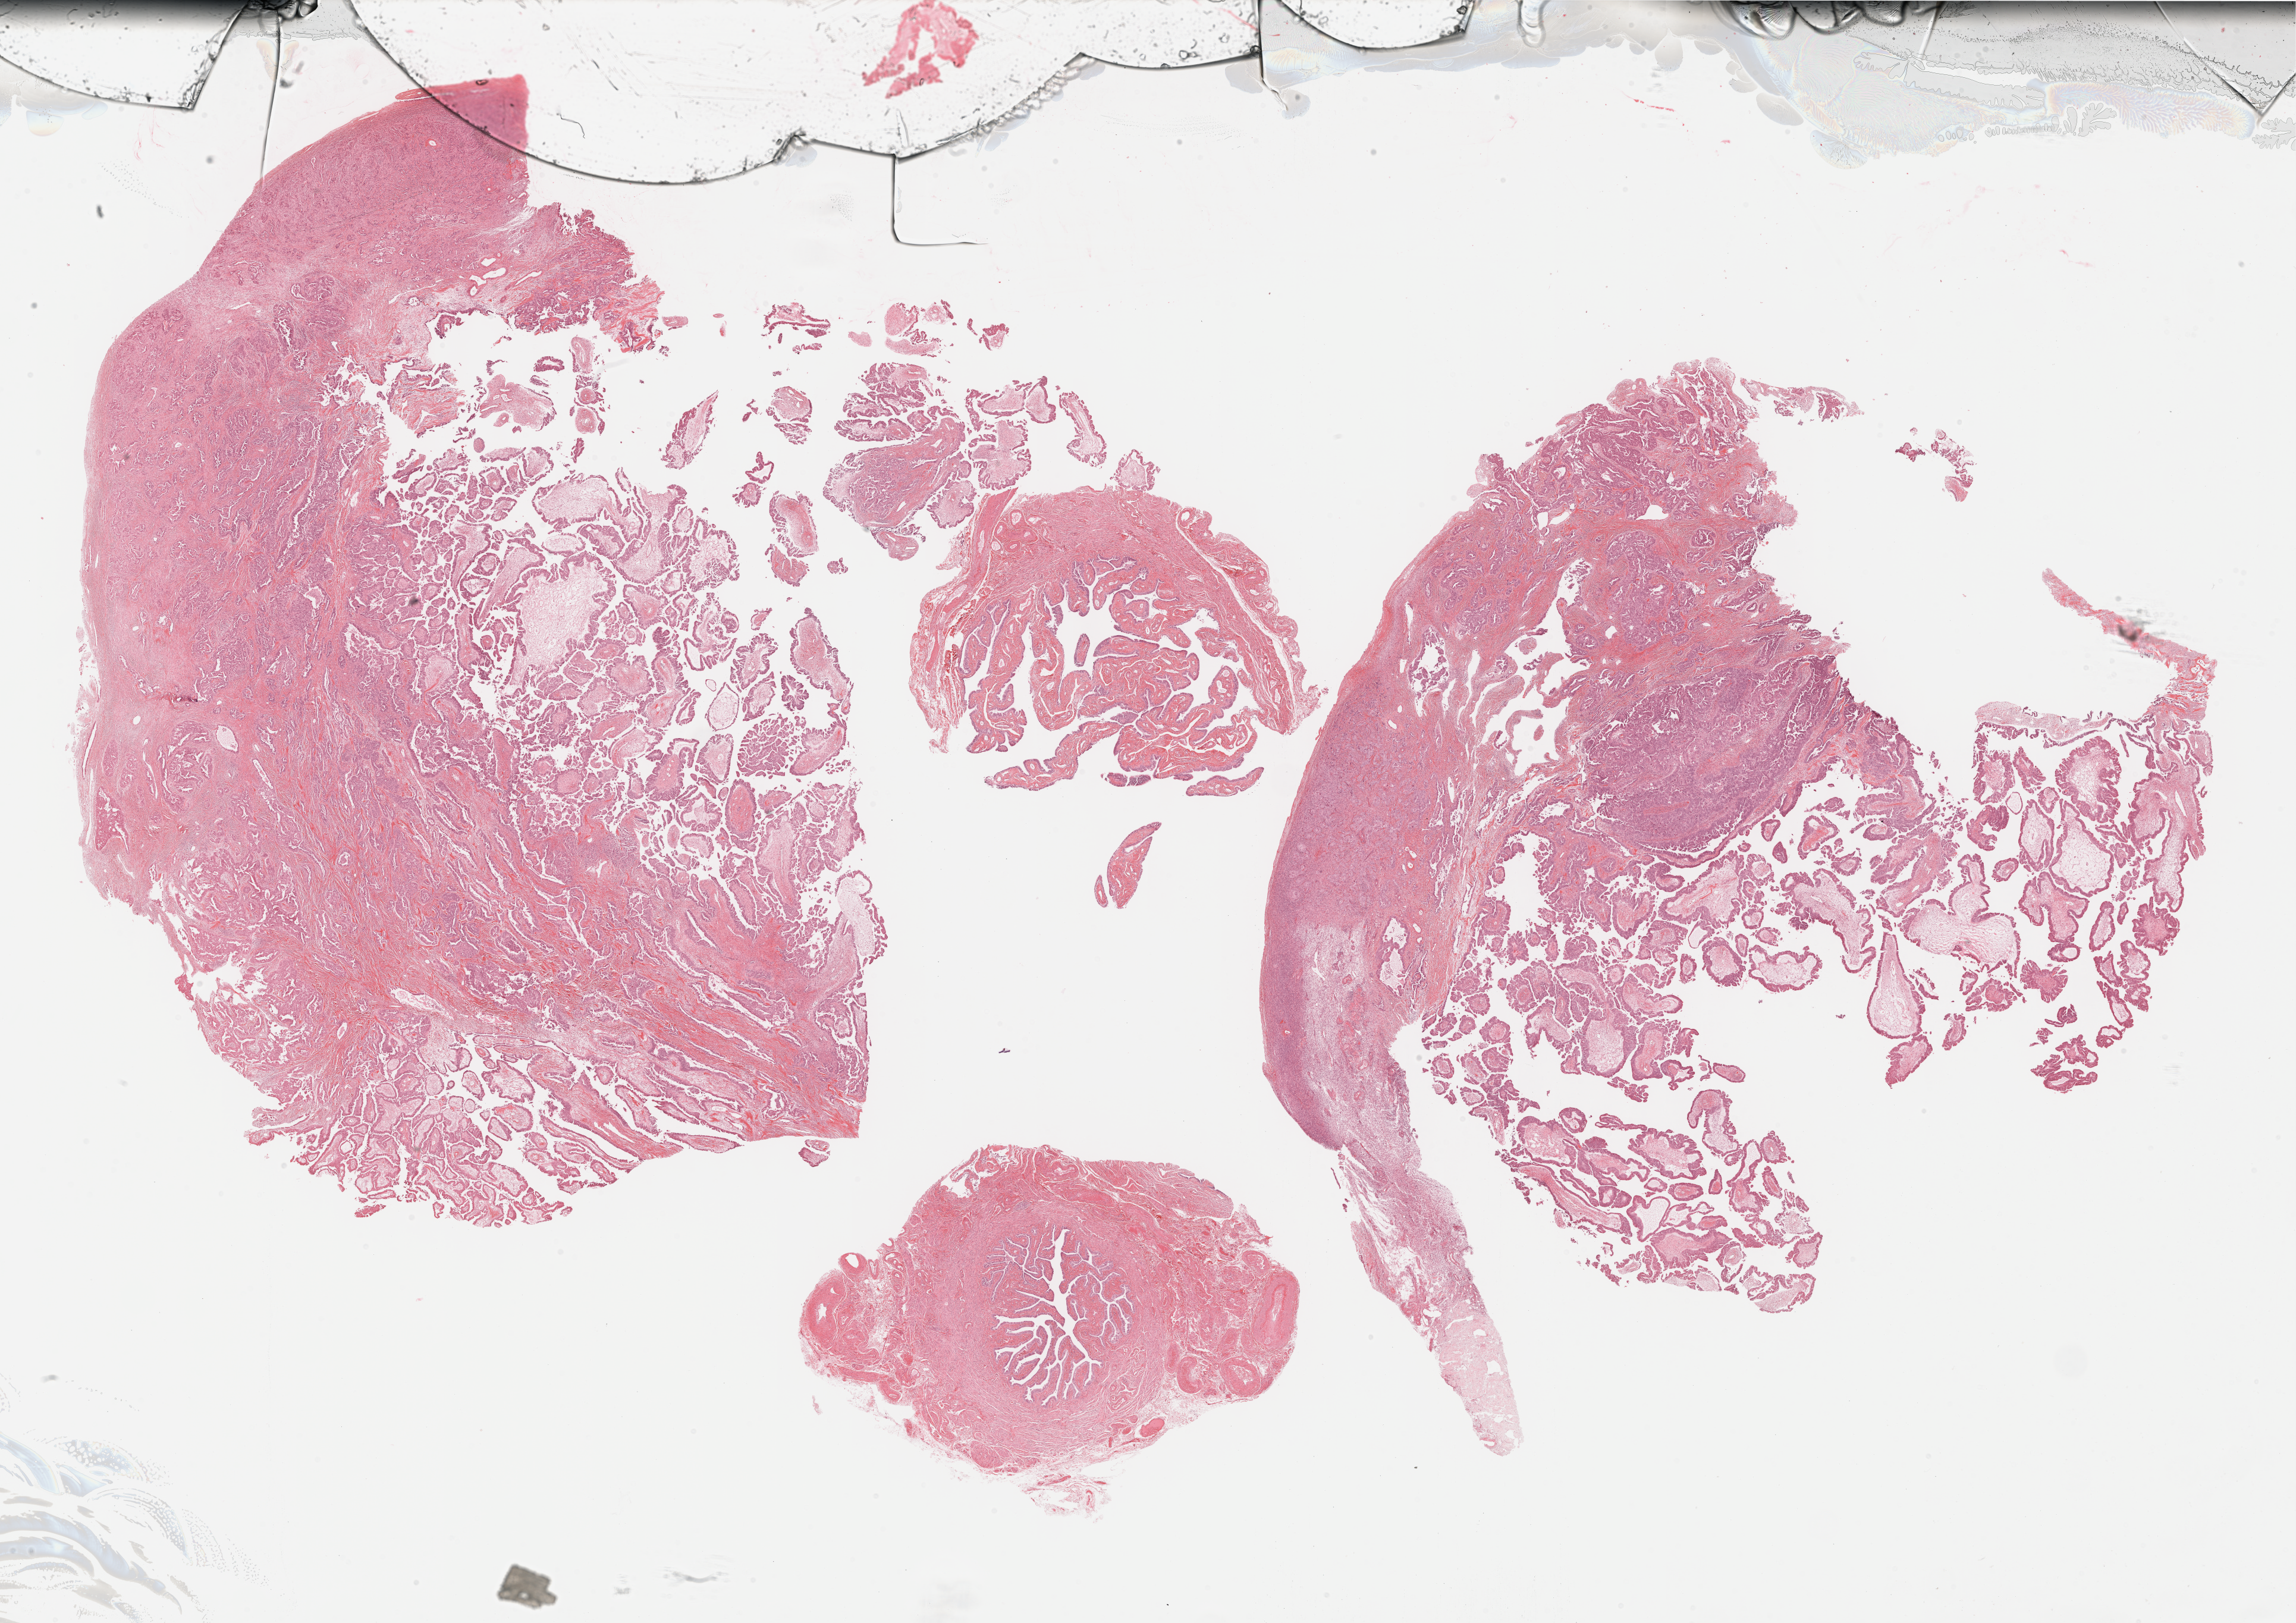
Hematoxylin and eosin (H&E) stained whole-slide image, whole scanned area (about 31.2 x 22.0 mm) shown as a low-resolution overview; formalin-fixed paraffin-embedded (FFPE) diagnostic section; sample: primary tumour, ovary. Patient: female, age at initial diagnosis 65 years. Histologic grade: G3 (poorly differentiated).
FIGO stage: IIIC. Histologic diagnosis: Serous cystadenocarcinoma, NOS.